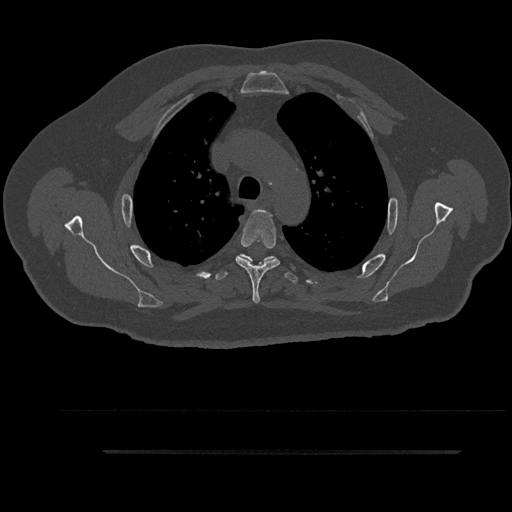
CT including the spine, one axial slice. Reconstruction kernel Br40s/3. Bone window (W 1800 / L 400 HU). 512 × 512 image matrix, field of view 432 × 432 mm. Patient: male, 63 years. Case-level facts recorded for this patient, not image findings: primary cancer: renal; vertebrae with lytic lesions (as recorded): T8.
Outlined on this slice (semi-automatically segmented with operator editing):
- T4 vertebra: box from (x=235, y=209) to (x=280, y=304) px
- T5 vertebra: (x=216, y=255)–(x=298, y=282)